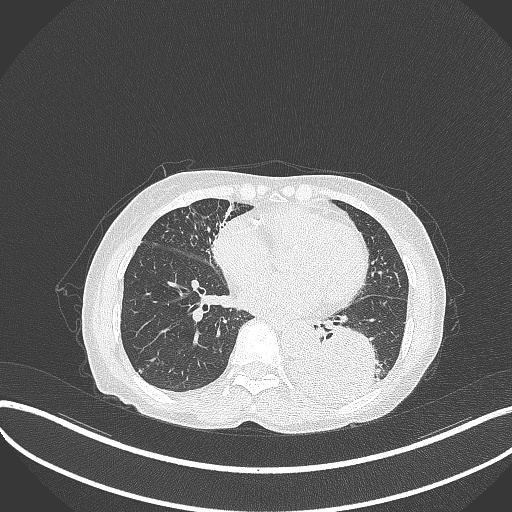
Chest CT, one axial slice. Position 117 of 370 along the scan axis. Reconstruction kernel B70f. Lung window (W 1500 / L -600 HU). 1 mm slice thickness. 512 × 512 image matrix, field of view 400 × 400 mm. Patient: female, 78 years. From the clinical record (not read from this slice): clinical TNM (as recorded): T3 N0 M1.
Structures marked on this image (rectangle marked by the reading radiologist):
- lung tumour (recorded histology: squamous cell carcinoma): box from (x=285, y=320) to (x=379, y=400) px